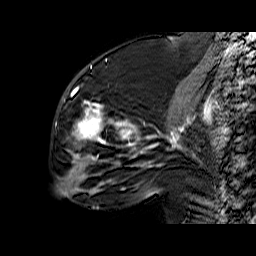
Breast MRI (dynamic contrast-enhanced), one sagittal slice; position 27 of 60 along the scan axis; dynamic contrast-enhanced series, time point 2 of 6 at this slice position (early post-contrast); 1.5 T; TE 6.4 ms, TR 32.9 ms; 4 mm slice thickness; 256 × 256 image matrix, field of view 200 × 200 mm. Female patient. From the clinical record (not read from this slice): setting: breast cancer imaged before/during neoadjuvant chemotherapy; receptor status: triple-negative.
Annotated regions visible in this slice (semi-automatically segmented with operator editing):
- analysis volume of interest (the breast-tissue region the enhancement analysis was run in; not a lesion): box from (x=57, y=65) to (x=159, y=174) px
- tumour enhancement mask (voxels above the 100 % enhancement threshold inside the analysis volume of interest): (x=73, y=89)–(x=159, y=167)